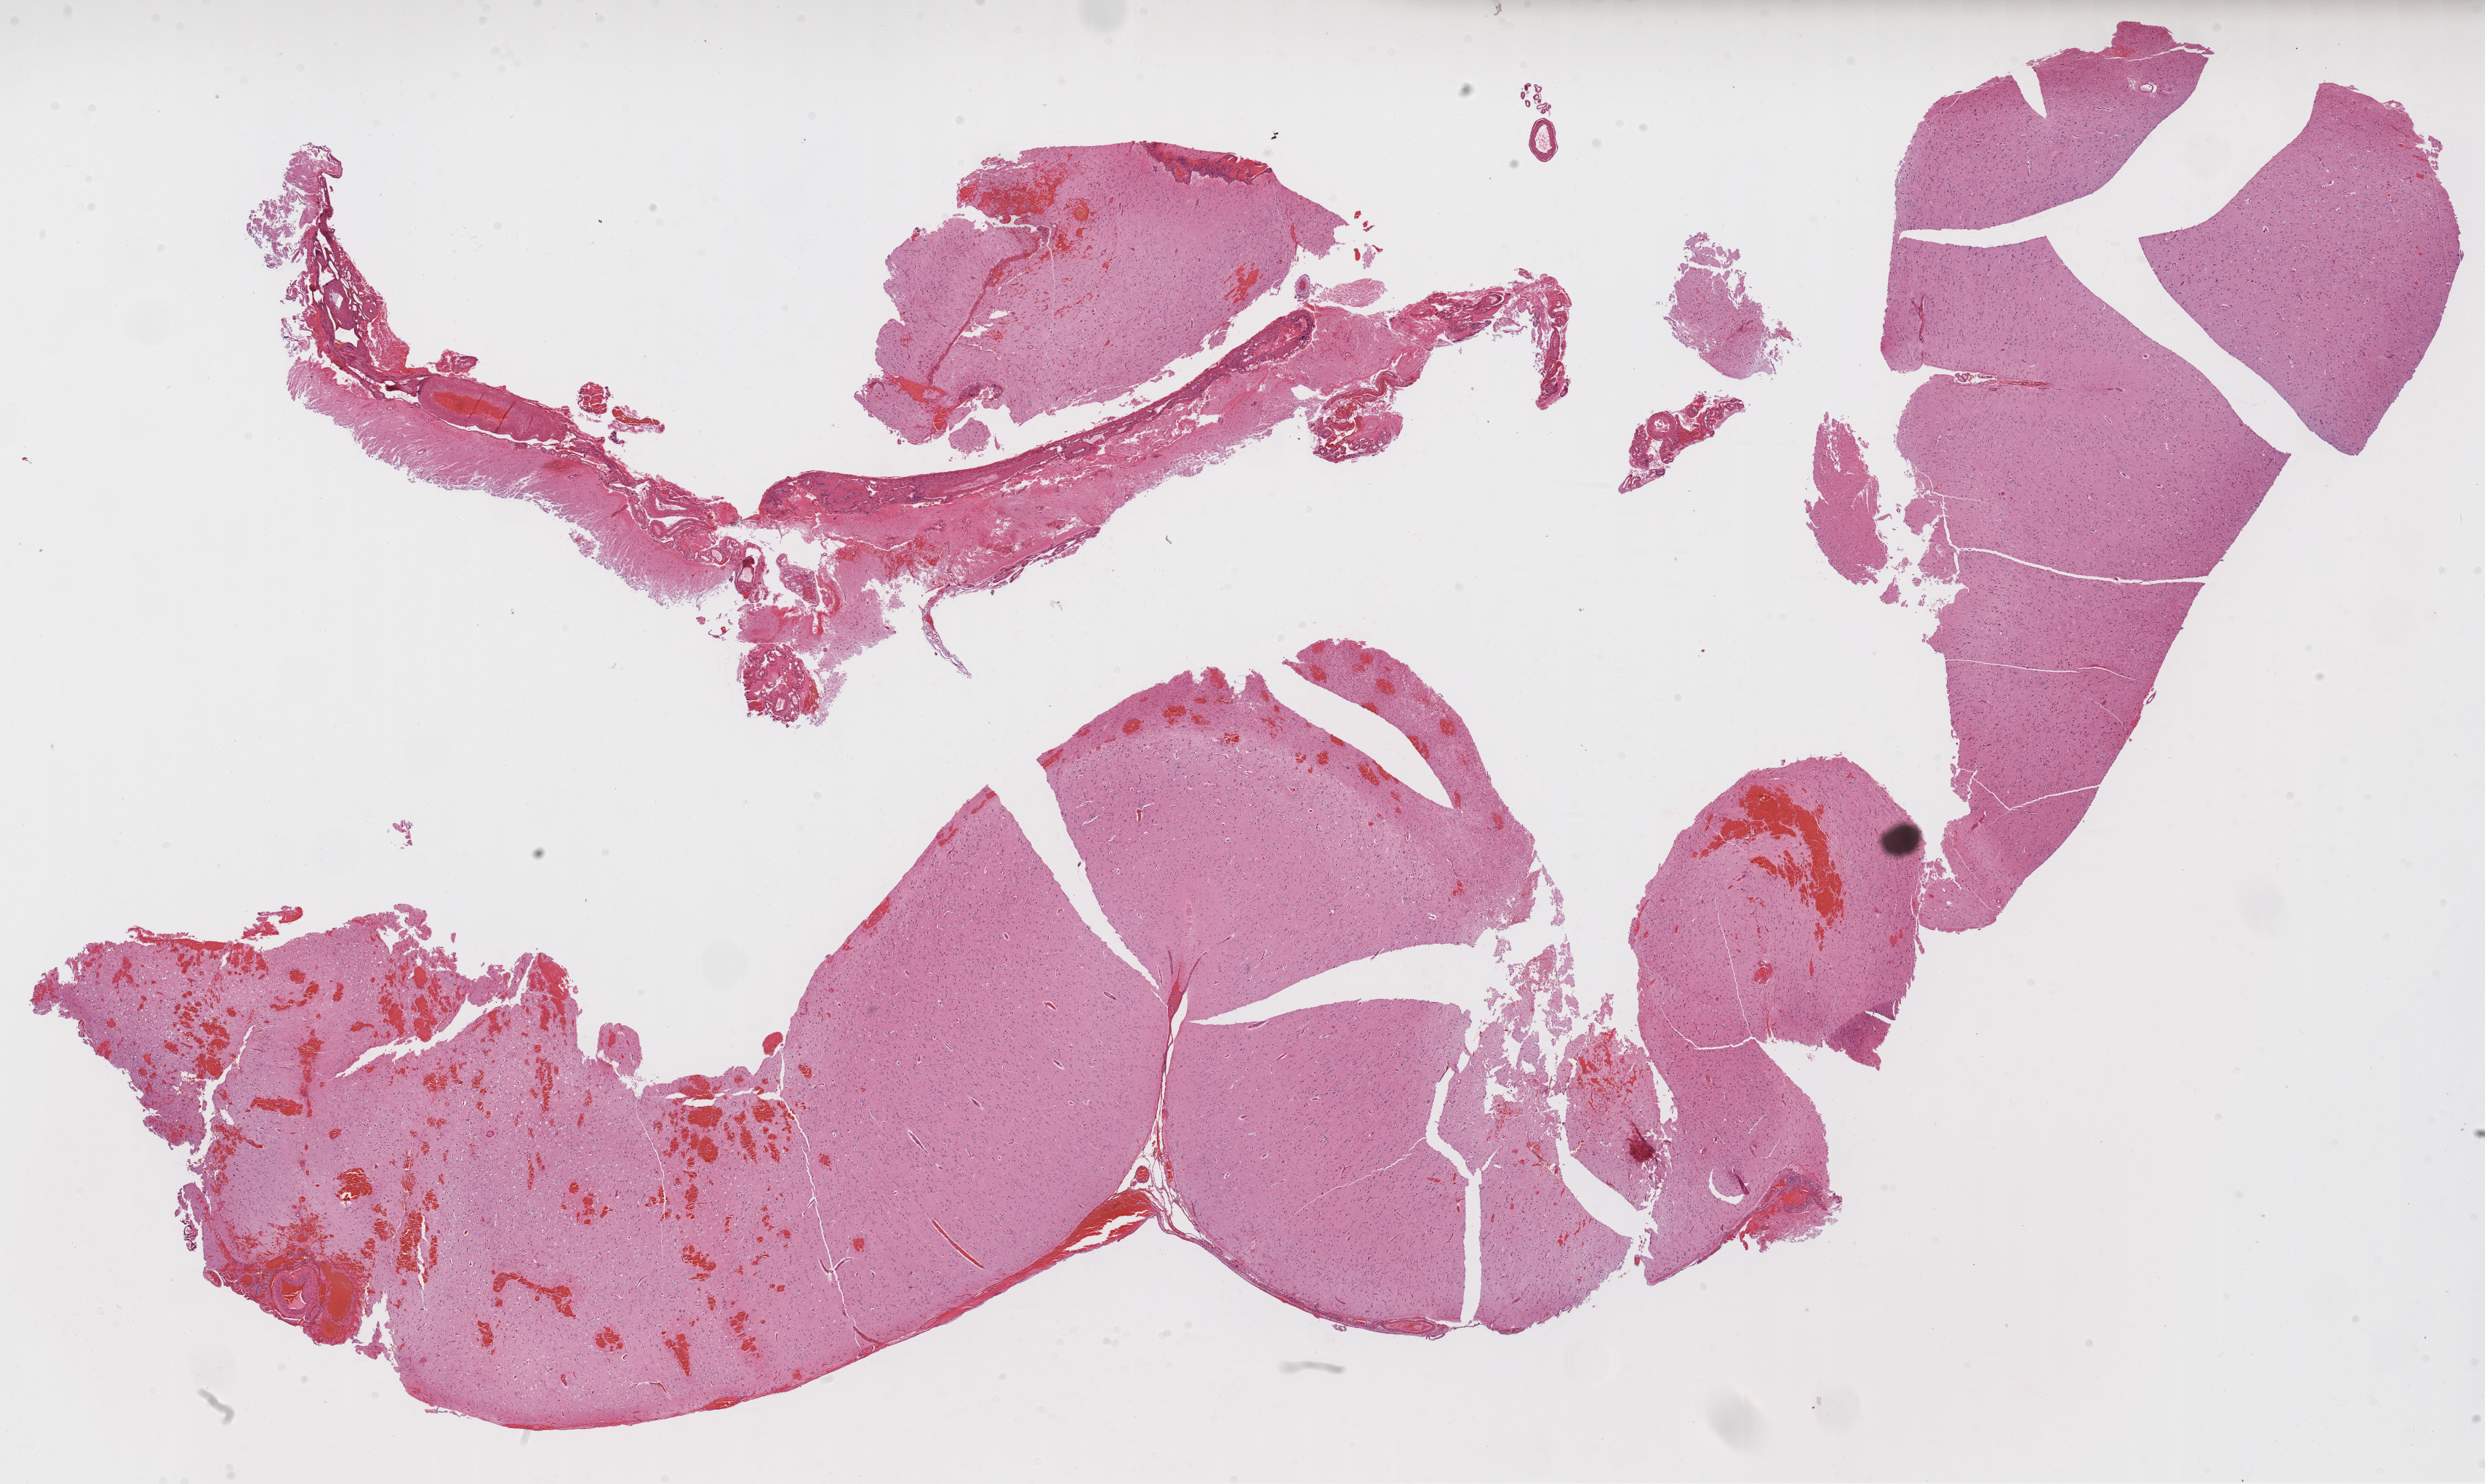
Whole-slide histology image, H&E — a low-resolution overview of the entire scanned area, about 27.6 x 16.5 mm (slide scanned at 20x). Formalin-fixed paraffin-embedded (FFPE) diagnostic section. Brain, primary tumour sample. Male patient; age at initial diagnosis 67 years.
Histologic diagnosis: Glioblastoma.